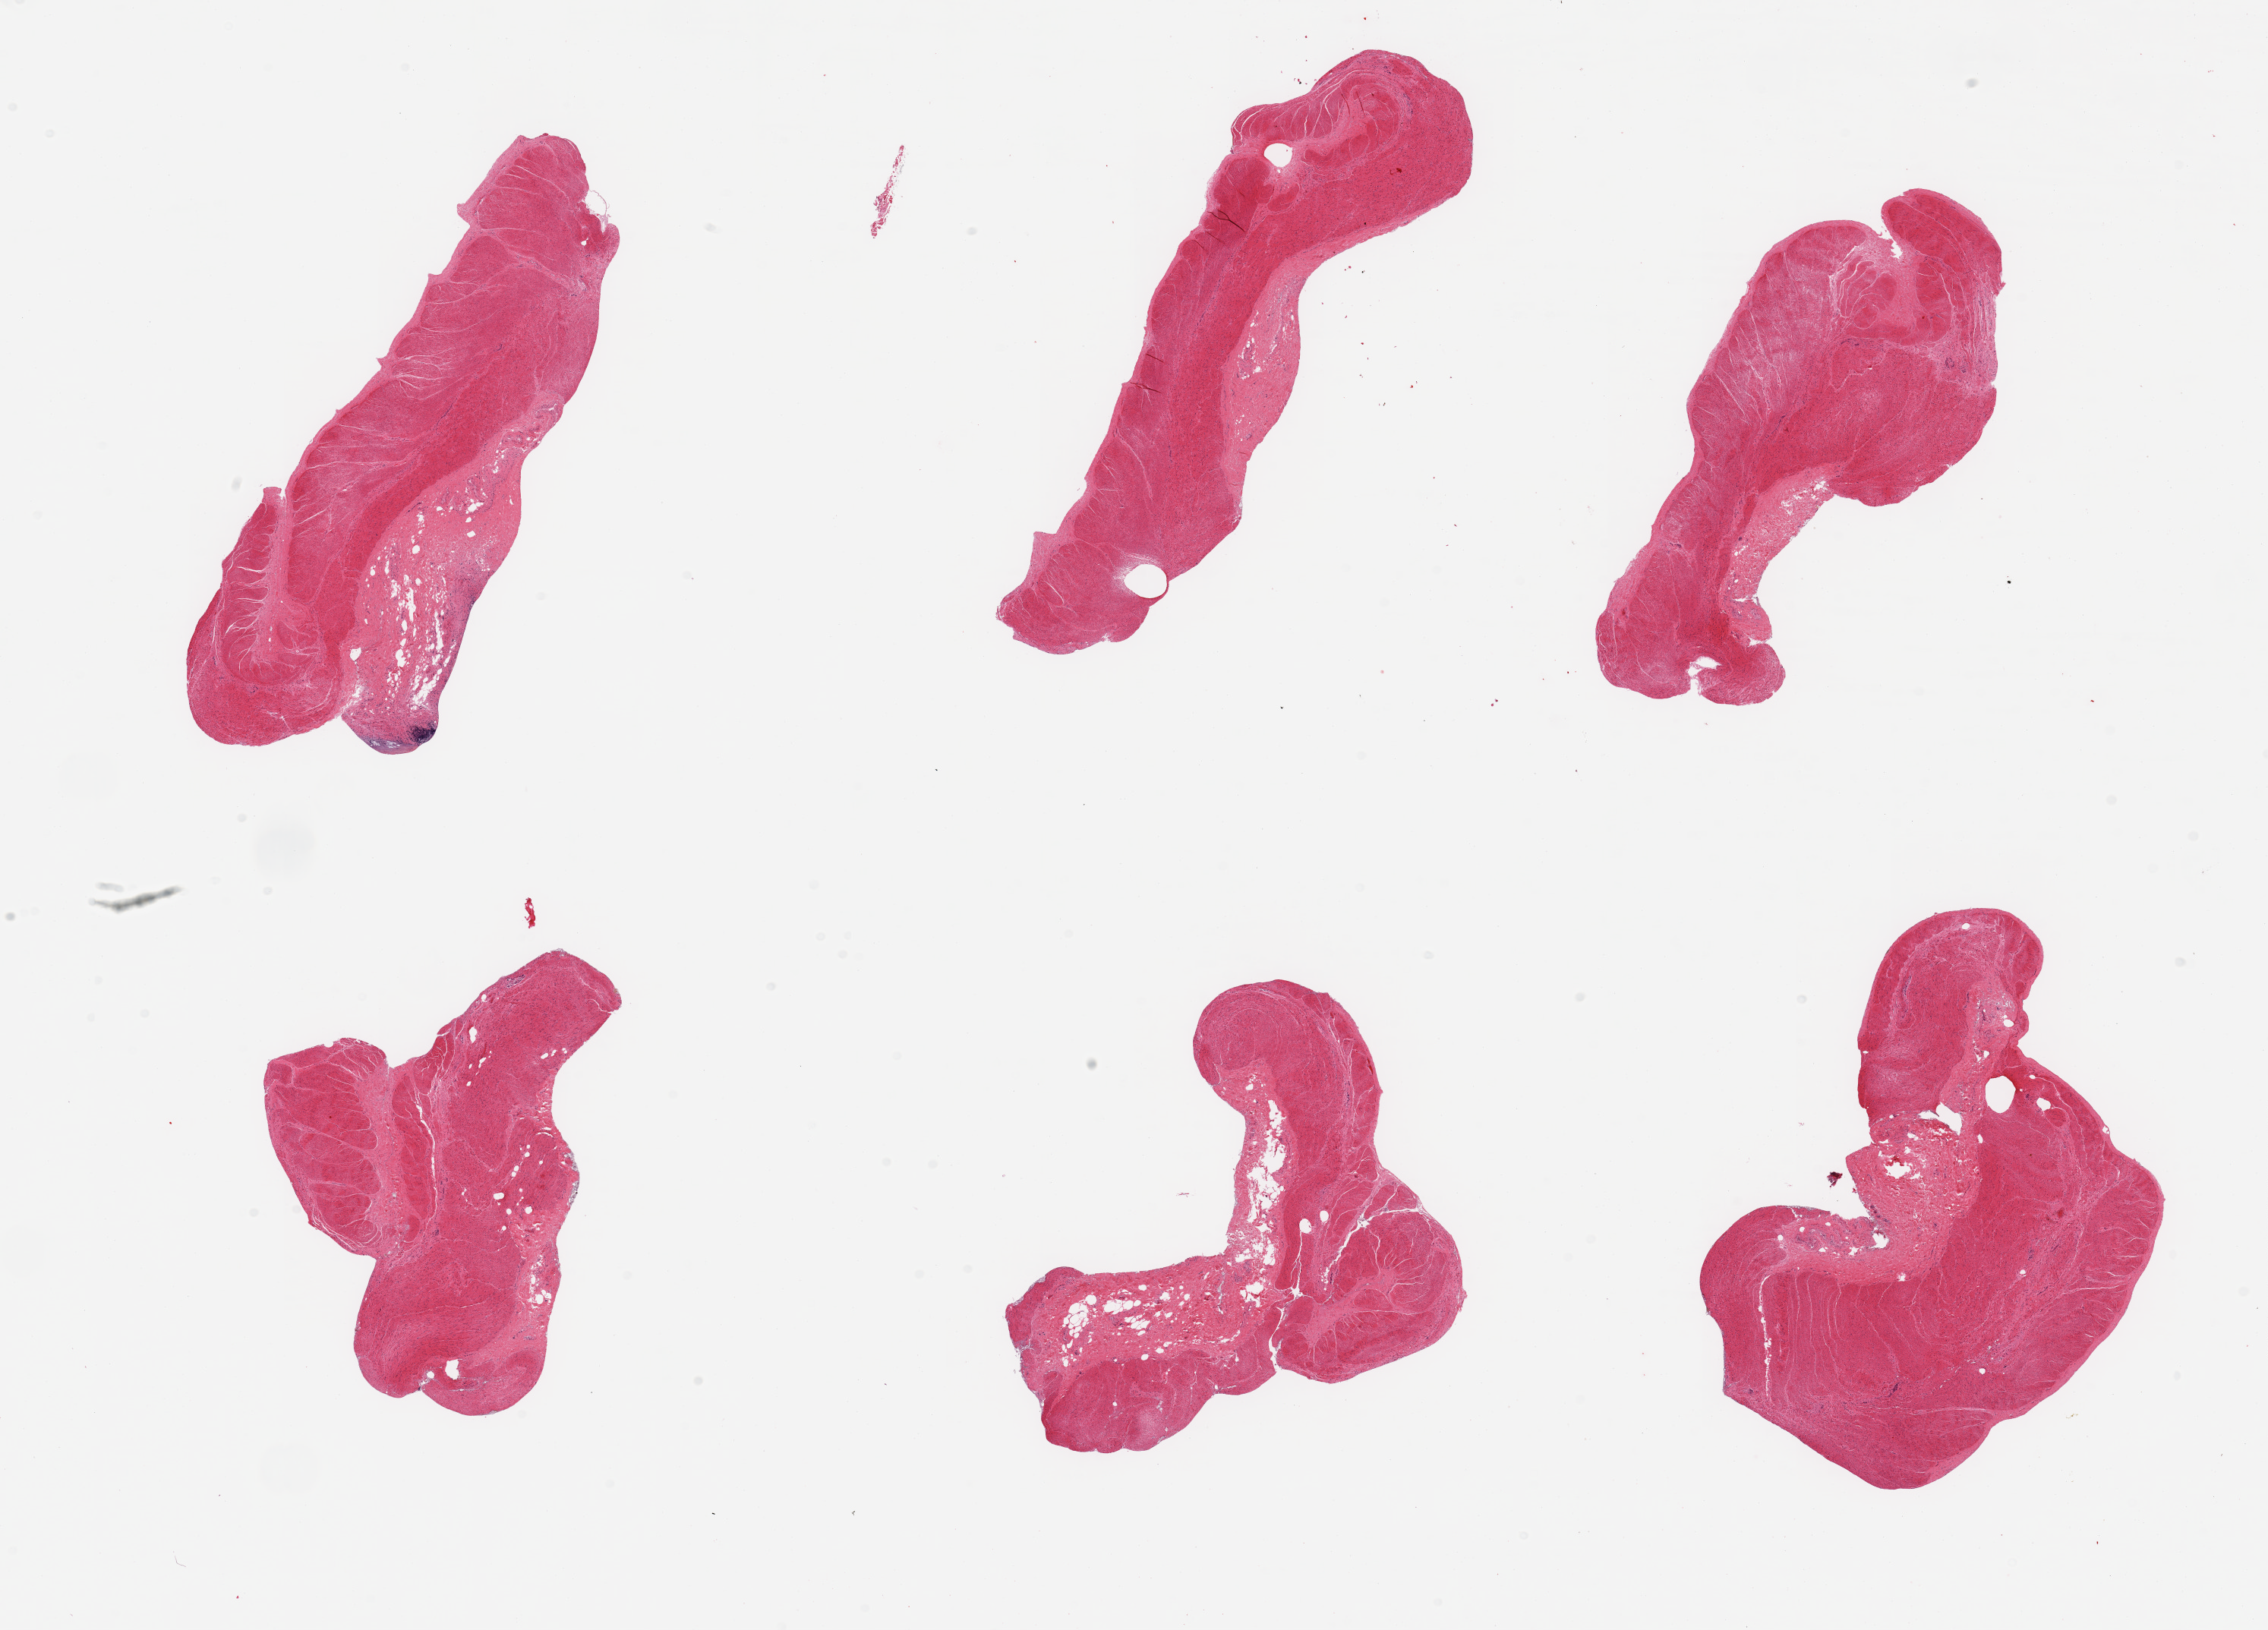
H&E whole-slide image, low-resolution overview of the scanned area, about 23.6 x 17.0 mm, PAXgene-fixed paraffin-embedded (PFPE) section, target tissue: sigmoid colon, donor tissue sample. Donor sex: male.
Reviewer comment on this tissue sample: 6 pieces, confirmed target muscularis; unusually advanced autolysis.